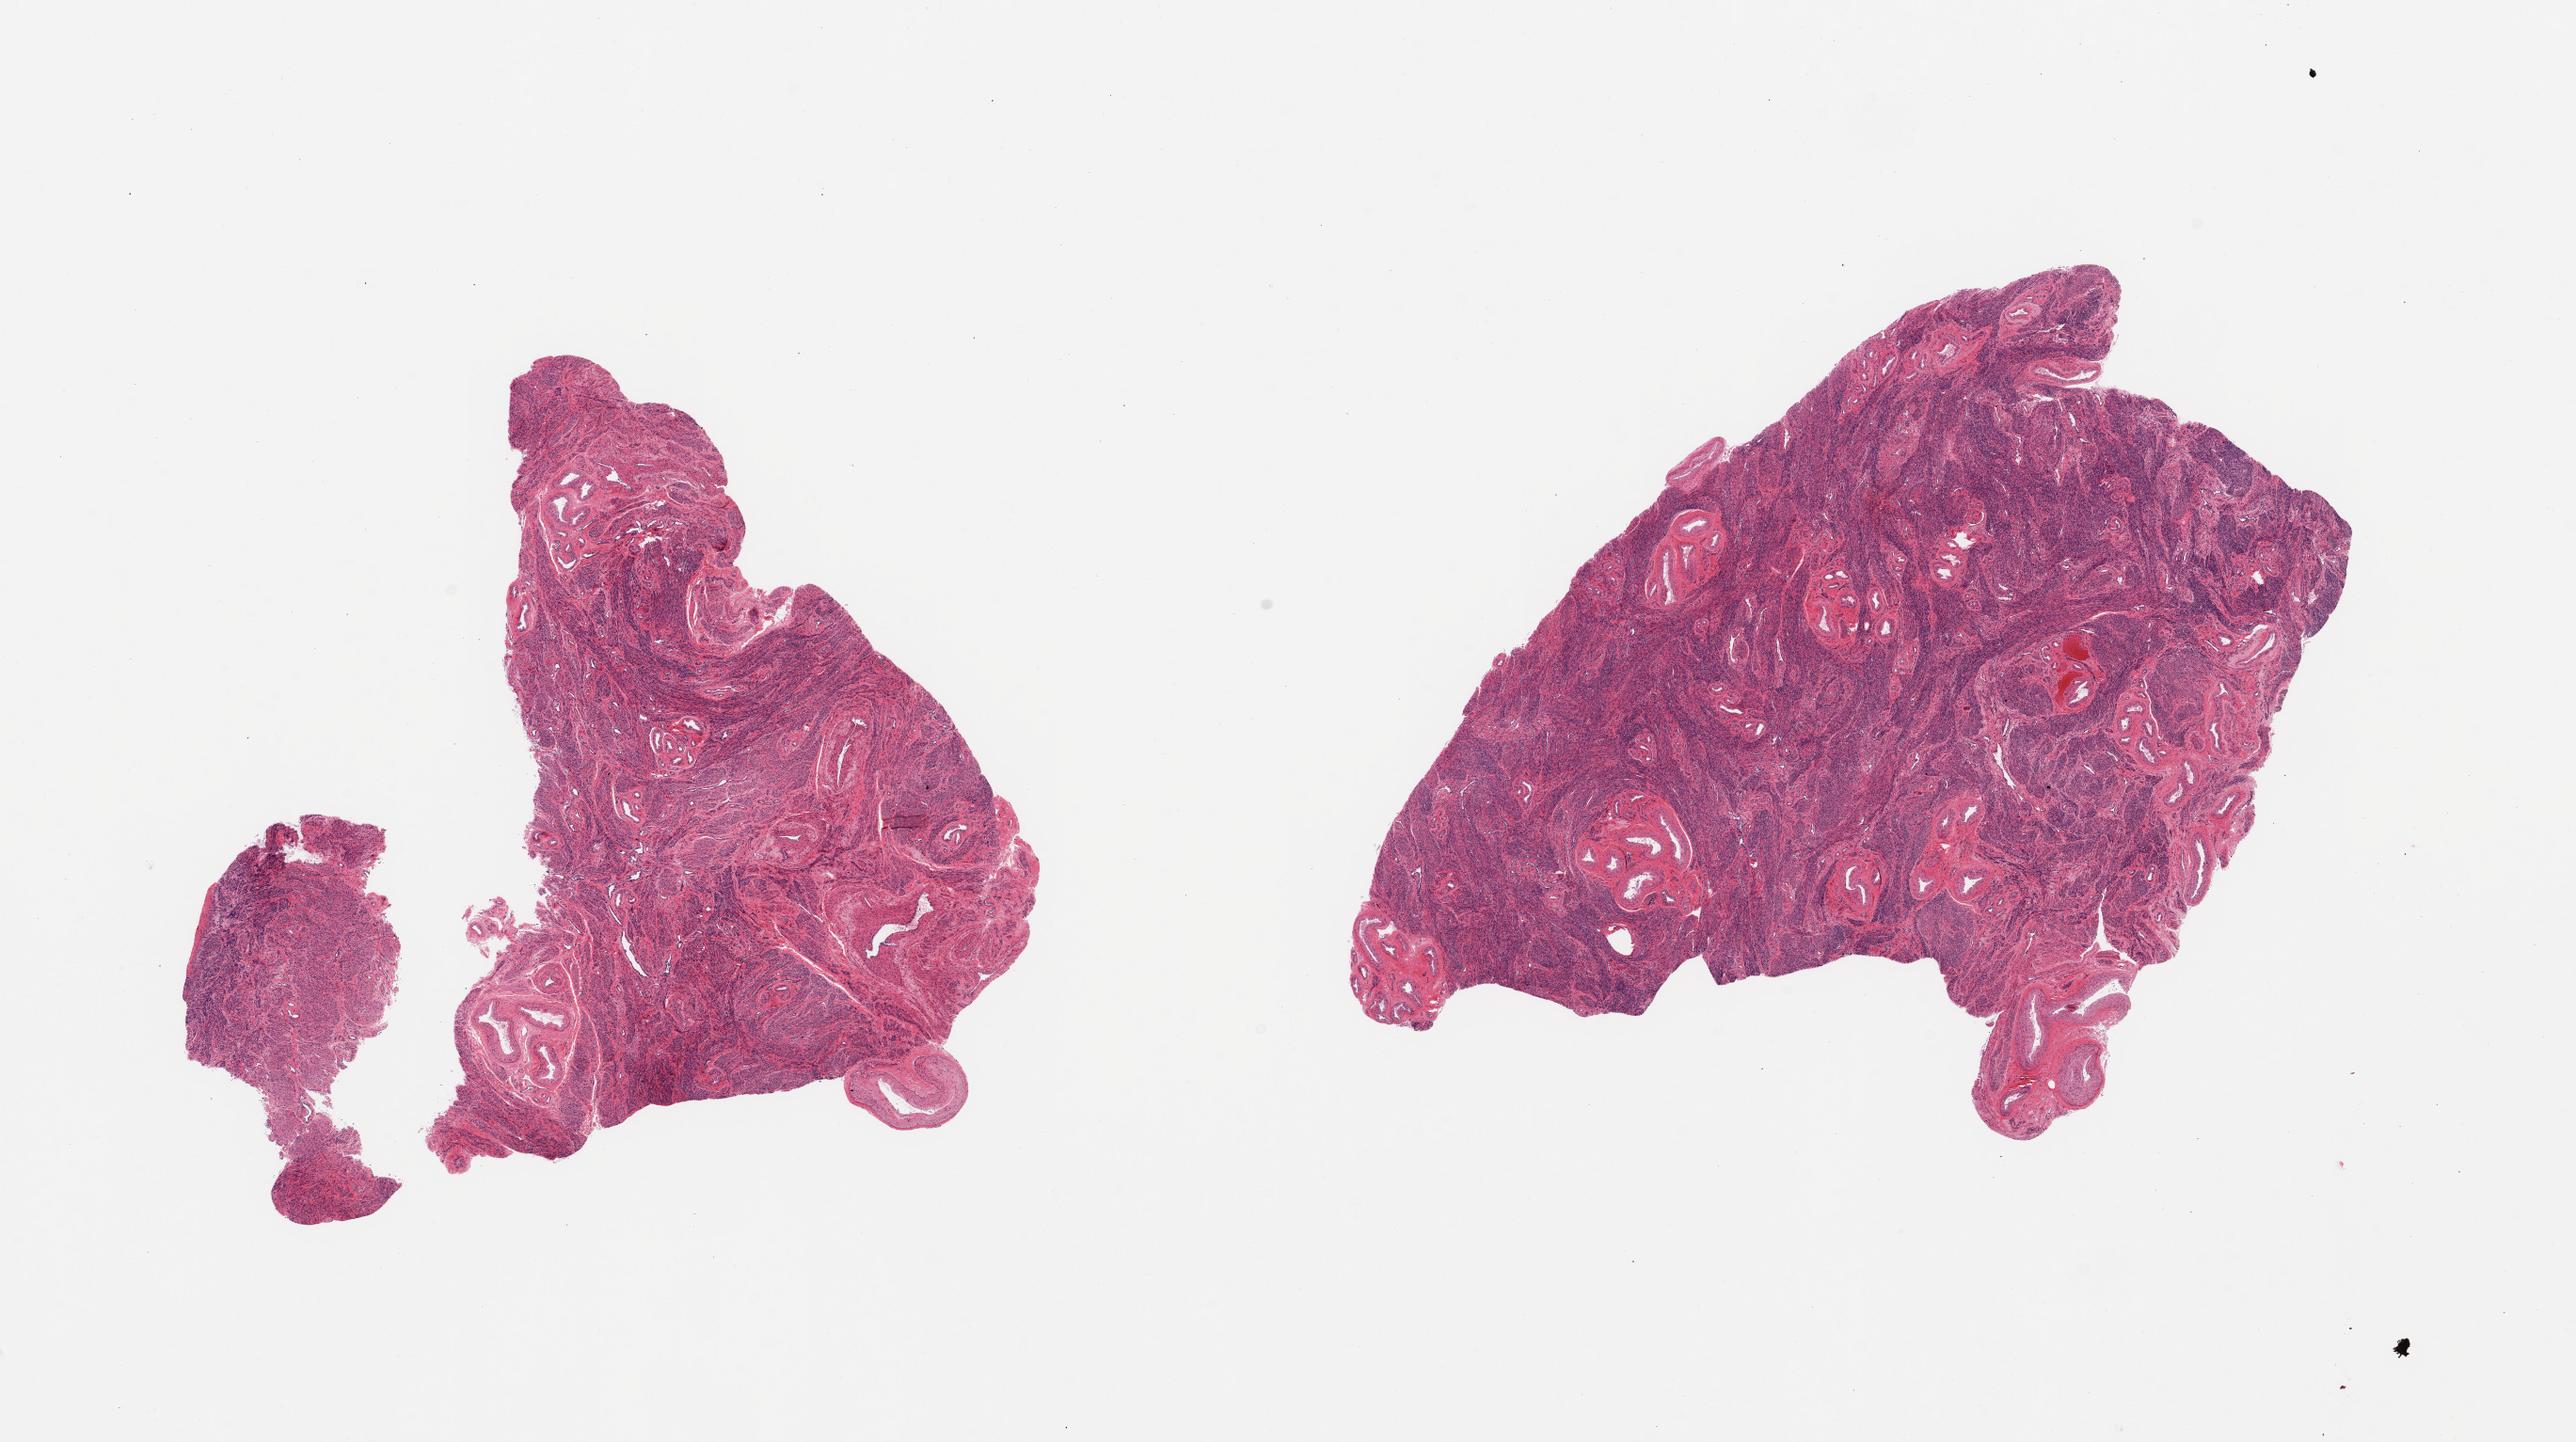
Digitized H&E-stained section, brightfield, whole scanned area (about 21.7 x 12.1 mm) shown as a low-resolution overview, PAXgene-fixed paraffin-embedded (PFPE) section, target tissue: uterus, tissue donor sample. Donor: female.
Reviewer comment on this tissue sample: 2 pieces; all myometrium.